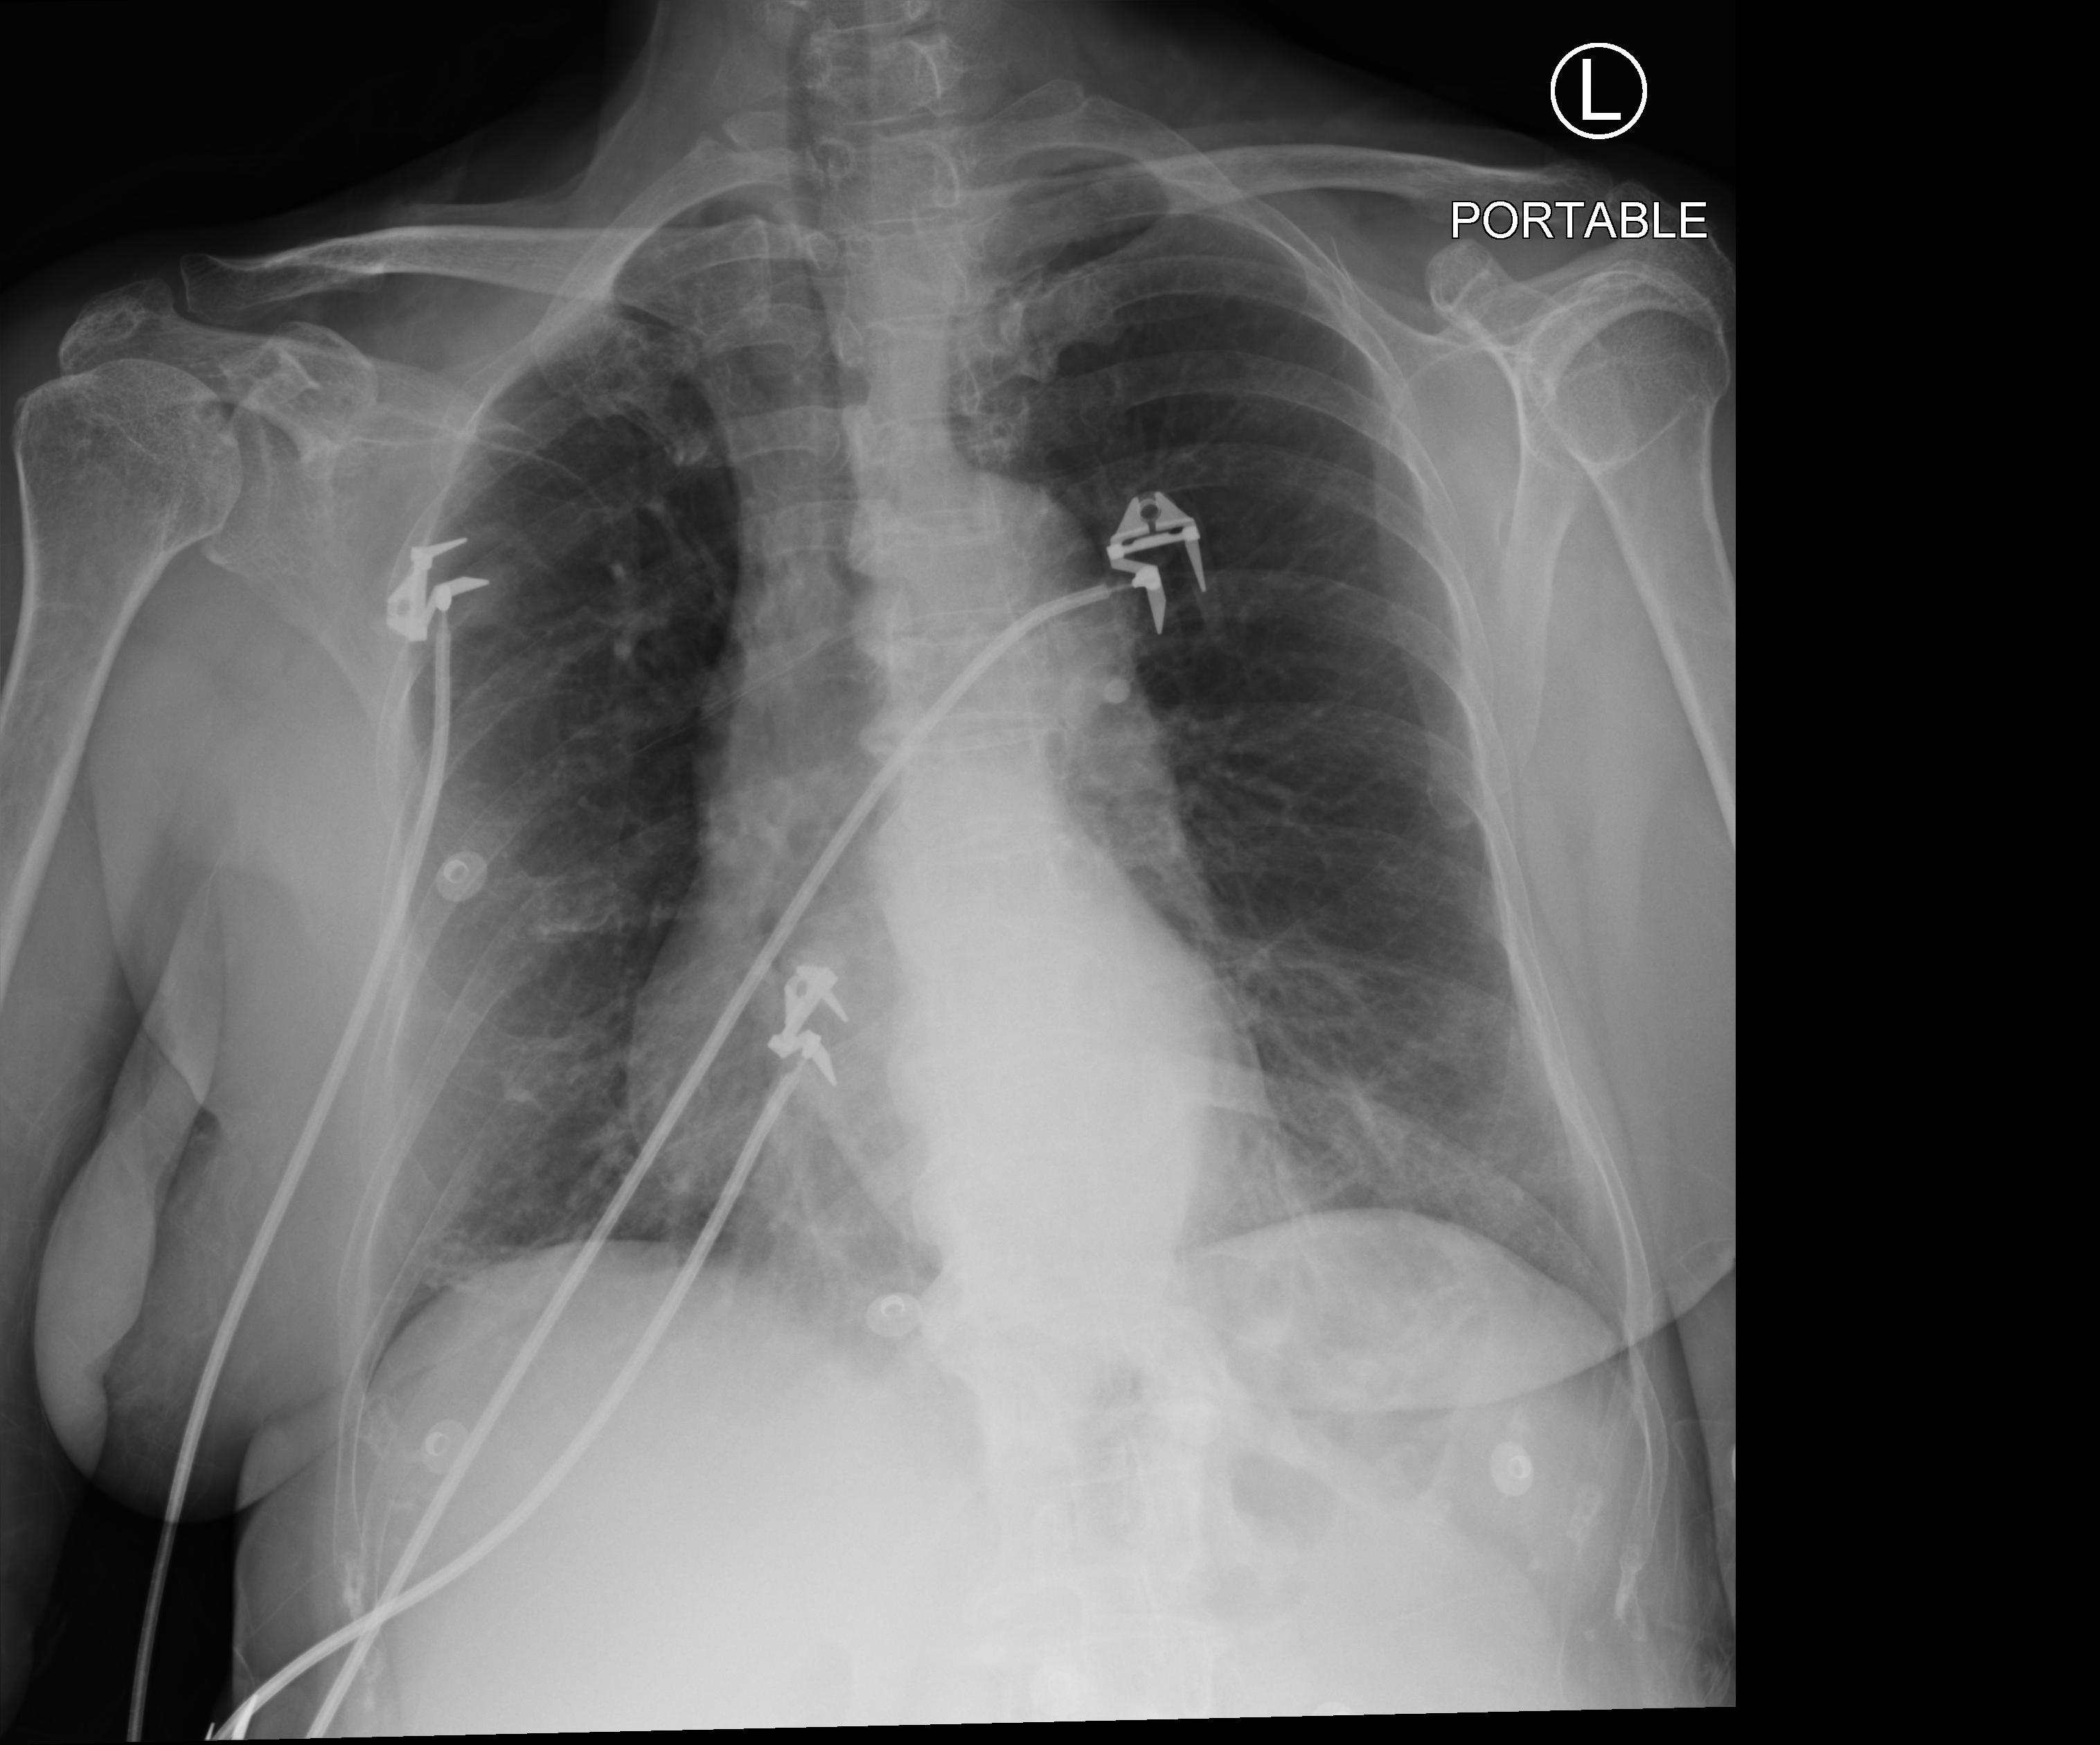
Chest X-ray (portable), anteroposterior (AP) projection. Female patient hospitalised with COVID-19, age 60–74 years.
From the hospital-stay record, not from the radiograph (when in the stay this image was taken is not recorded): hypertension (admission record): yes; admitted to intensive care during this hospital stay: no; mechanically ventilated during this hospital stay: no.